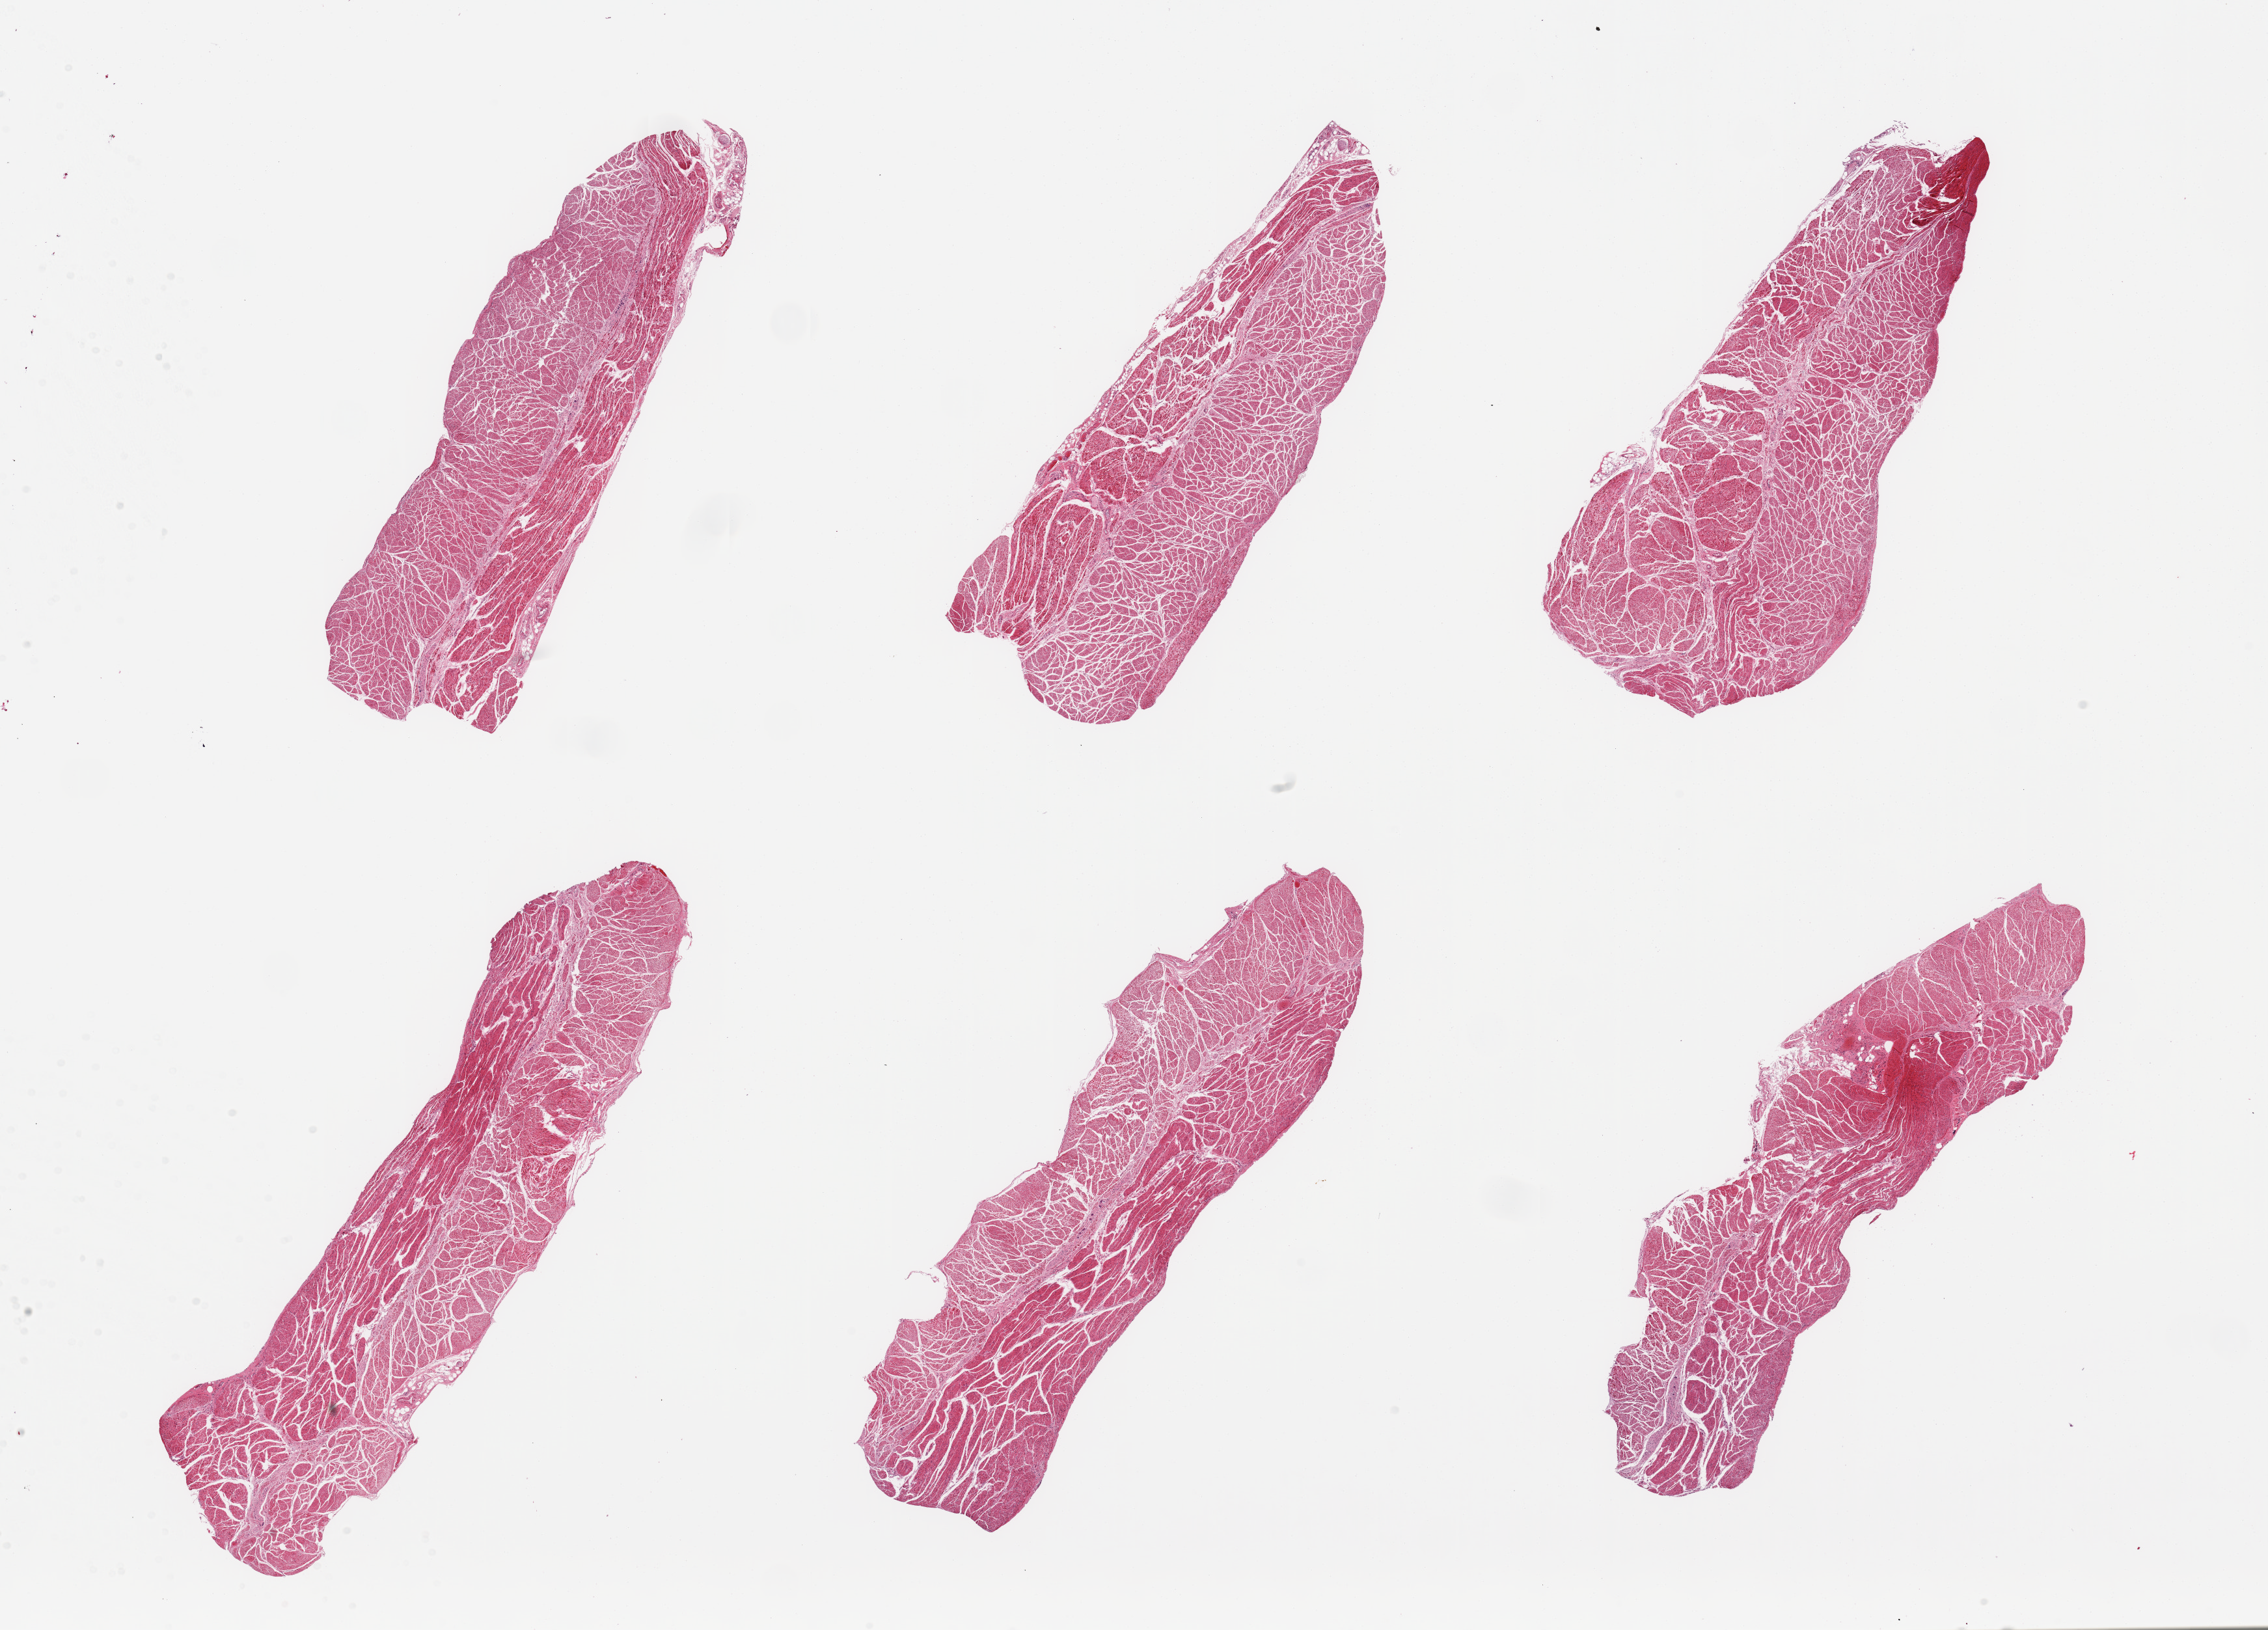
Whole-slide image, hematoxylin and eosin (H&E) stain — a low-resolution overview of the entire scanned area, about 27.6 x 19.8 mm (slide scanned at 20x); PAXgene-fixed paraffin-embedded (PFPE) section; target tissue: esophageal muscle; tissue donor sample. Donor sex: male.
• review note (as recorded): 6 pieces; well dissected muscularis, but not well preserved